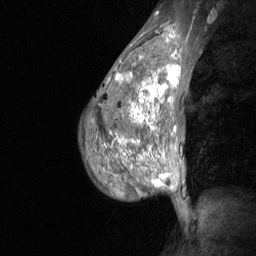
Breast MRI (dynamic contrast-enhanced), one sagittal slice; slice 44 of 64 in the series (ordered by position); dynamic contrast-enhanced study with each time point stored as its own series, time point 2 of 3 at this slice position (early post-contrast, ordered by acquisition time); 1.5 T; TE 4.8 ms, TR 27 ms; 256 × 256 image matrix. Female patient, age 36 years. Case-level facts recorded for this patient, not image findings: setting: breast cancer imaged before/during neoadjuvant chemotherapy; receptor status: HR-positive, HER2-negative.
Annotated regions visible in this slice (semi-automatic segmentation, software-assisted and operator-edited):
- analysis volume of interest (the breast-tissue region the enhancement analysis was run in; not a lesion): bounding box <79,45,187,210> (left, top, right, bottom; pixels)
- tumour enhancement mask (voxels above the 90 % enhancement threshold inside the analysis volume of interest): <116,51,181,185>